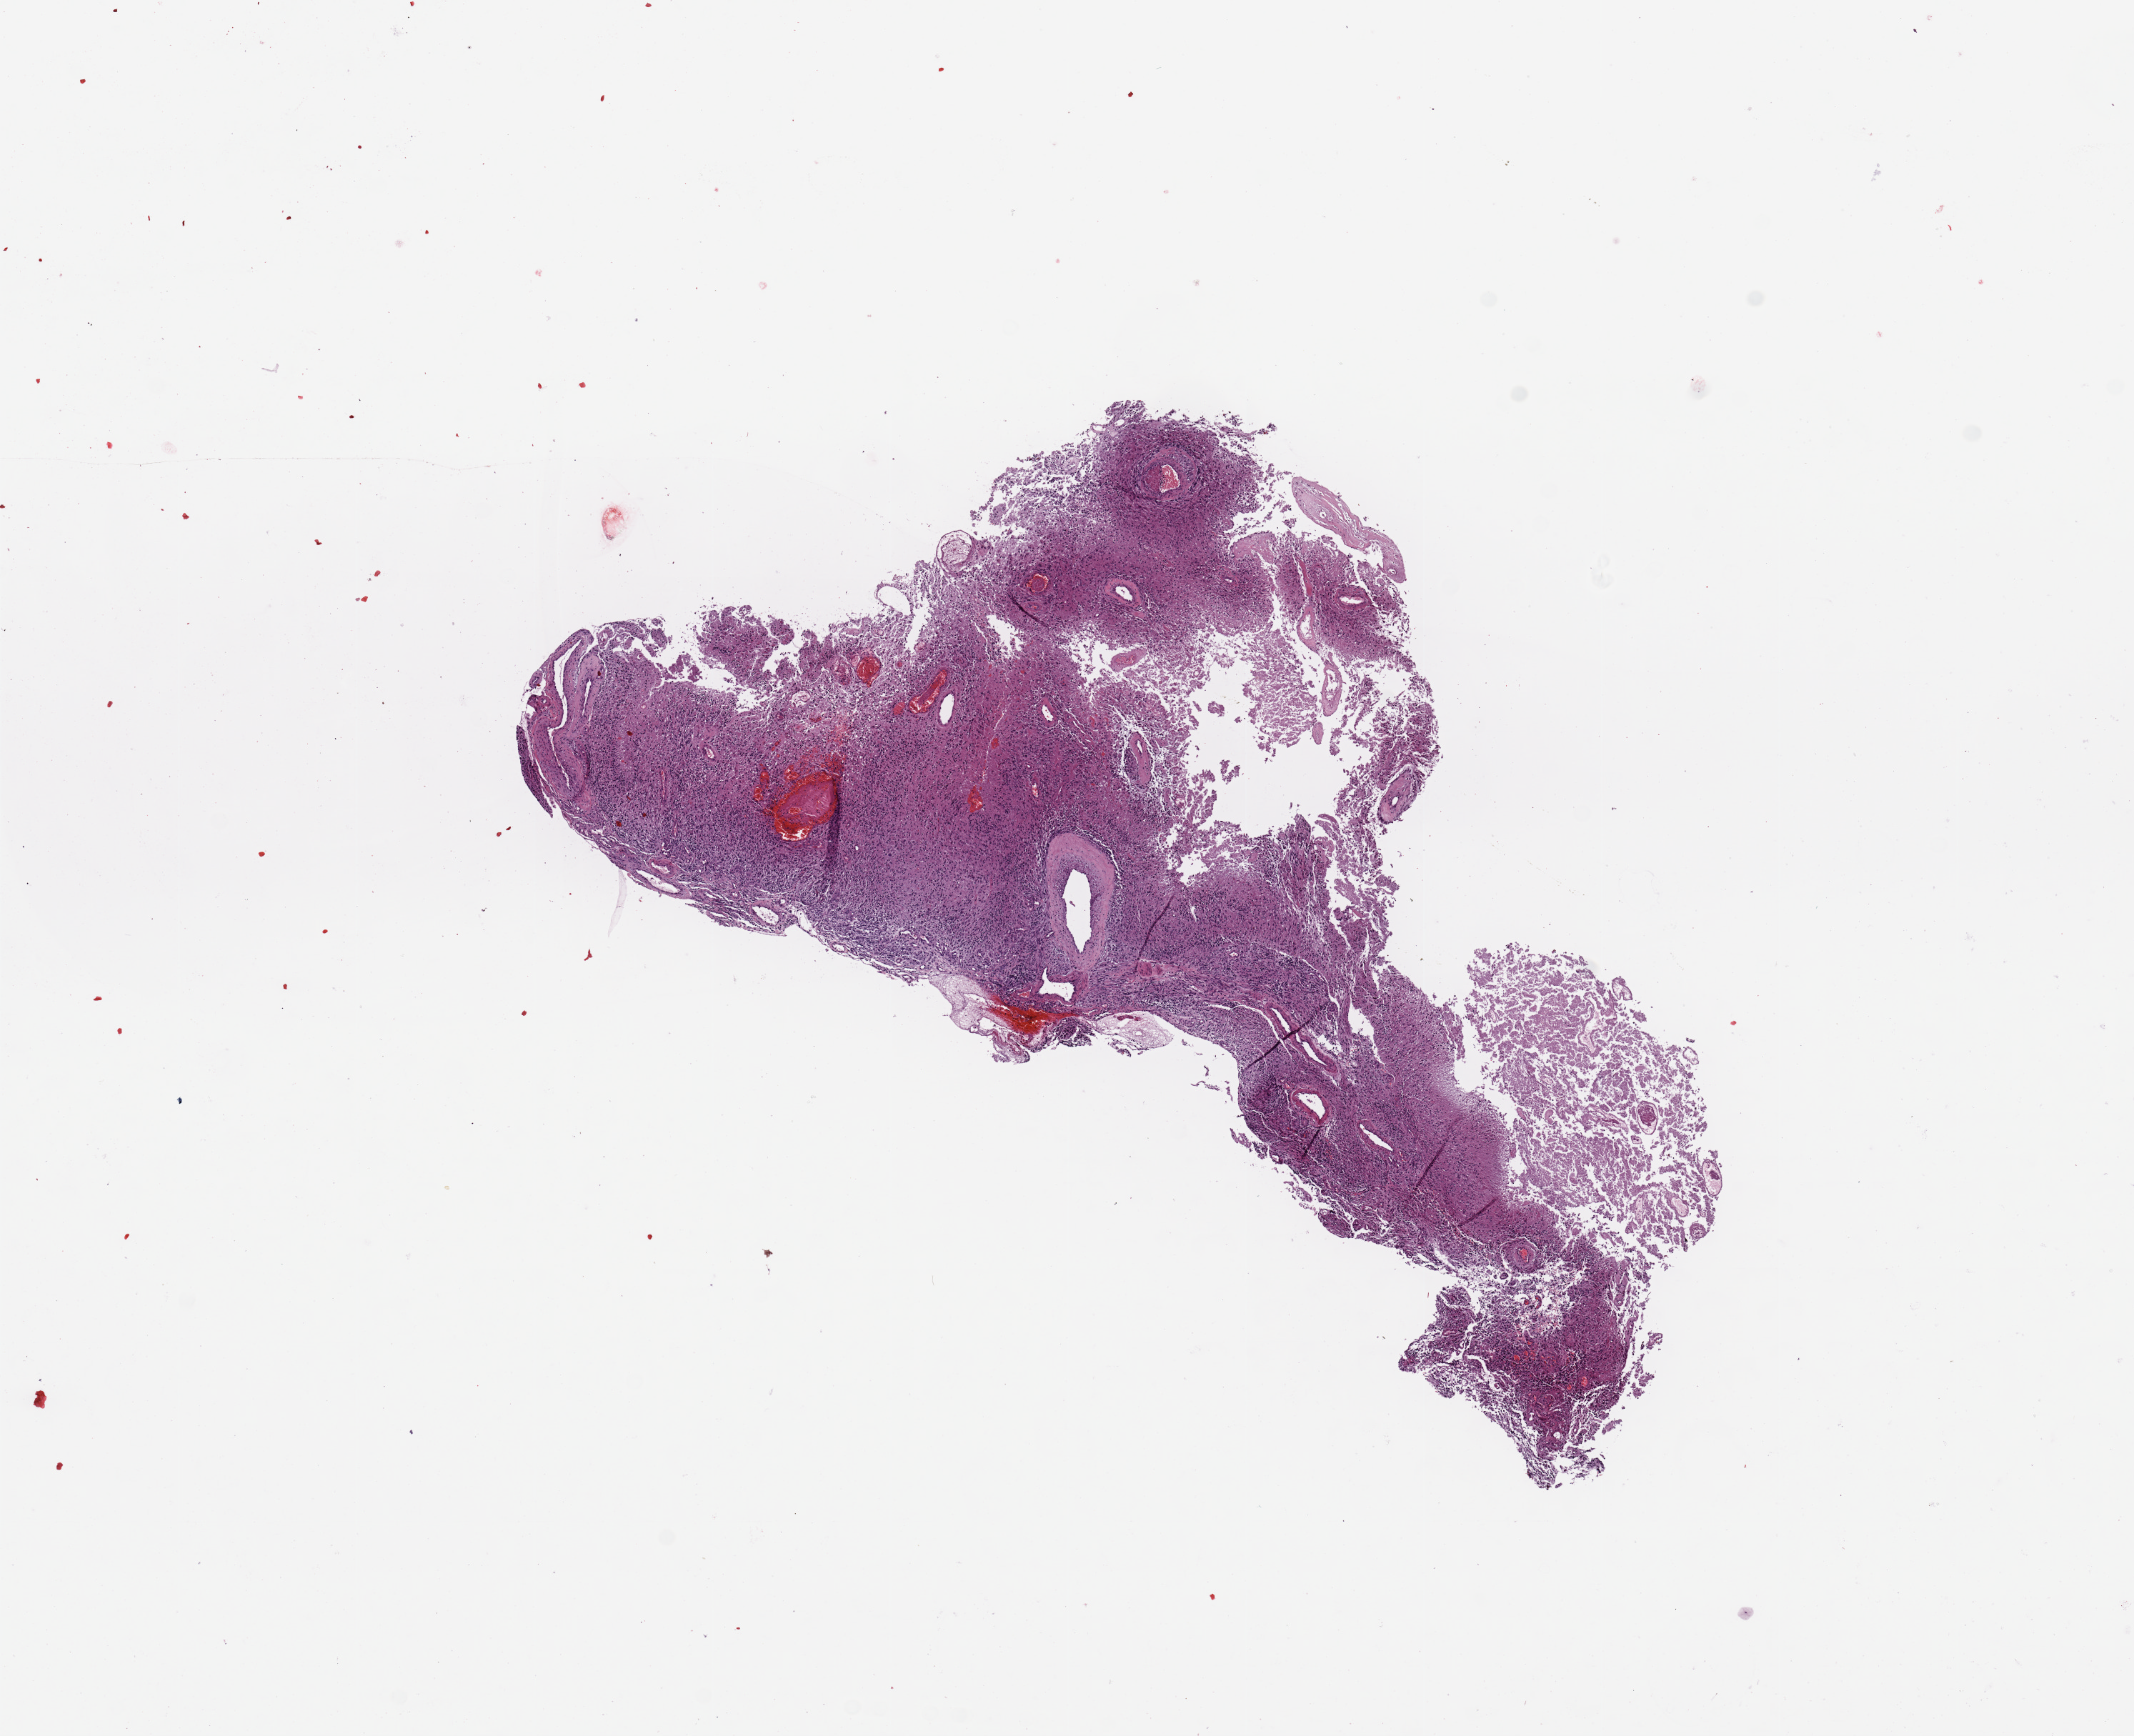
Whole-slide histology image, H&E-stained, whole scanned area (about 11.8 x 9.6 mm, slide scanned at 20x) shown as a low-resolution overview. Brain, tumour tissue. Patient: male, age 69 years.
* histologic diagnosis: Glioblastoma